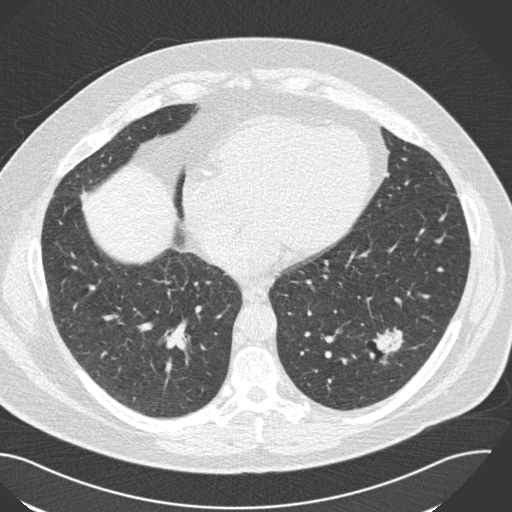
Low-dose screening chest CT, one axial slice. Position 68 of 153 along the scan axis. 120 kVp. Lung window (W 1500 / L -600 HU). 512 × 512 image matrix, field of view 394 × 394 mm.
Outlined on this slice (manually delineated by an expert):
- lesion 1 (tumor, lower lobe of left lung): box from (x=374, y=330) to (x=403, y=364) px